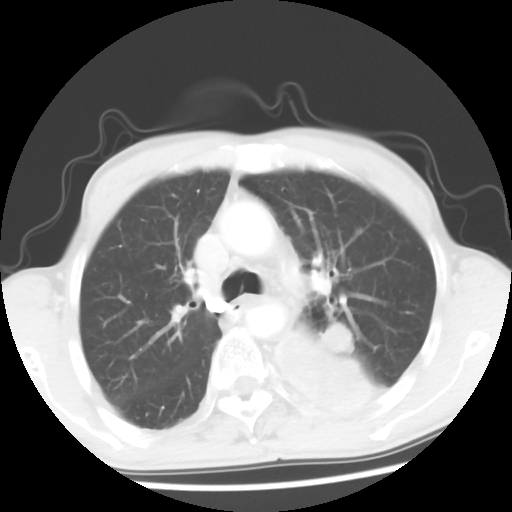
Chest CT, one axial slice. Slice 39 of 56 in the series (ordered by position). 120 kVp. Lung window (W 1500 / L -600 HU). 5 mm slice thickness. 512 × 512 image matrix, field of view 318 × 318 mm. Male patient, age 60 years. From the clinical record (not read from this slice): clinical TNM (as recorded): T4 N0 M0.
Annotated regions visible in this slice (bounding box drawn by a radiologist):
- lung tumour (recorded histology: squamous cell carcinoma): bounding box (x1, y1, x2, y2) in pixels: (263, 324, 395, 416)